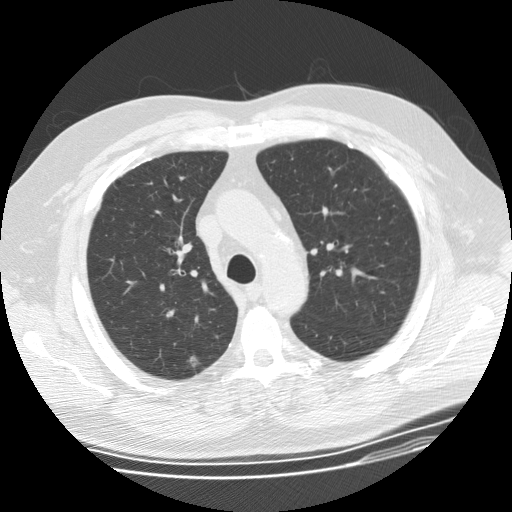
Axial slice from a low-dose chest CT screening exam, third annual screen, lung window (W 1500 / L -600 HU), 2.5 mm slice thickness, standard (soft-tissue) reconstruction kernel (STANDARD), 512 × 512 image matrix. Male, age 62 years at enrolment. Former smoker at enrolment.
- Expert-annotated lung lesion, bounding box <171,348,211,381> (left, top, right, bottom; pixels).
- Screening reader's record for this exam (one nodule recorded; not confirmed to be the boxed lesion): non-calcified nodule or mass ≥4 mm, right upper lobe, 10 × 10 mm, poorly defined margins, ground glass attenuation, pre-existing on the prior screen: yes; interval growth: yes.
- Official screen result: positive, other.
- Participant outcome: lung cancer diagnosed 48 days after this screen — bronchiolo-alveolar adenocarcinoma, NOS, right upper lobe, well differentiated (G1), stage IA (AJCC 6th edition), 12 mm at pathology.